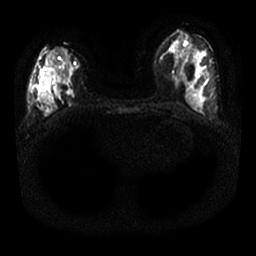
Breast MRI, one axial slice; slice 9 of 25 in the series (ordered by position); diffusion-weighted series; image 2 of 4 stored at this slice position (different b-values; order by instance number); 1.5 T; 4 mm slice thickness; 256 × 256 image matrix, field of view 330 × 330 mm. Female patient.
Annotated regions visible in this slice (expert manual segmentation):
- tumour on diffusion-weighted imaging: box from (x=64, y=83) to (x=71, y=97) px